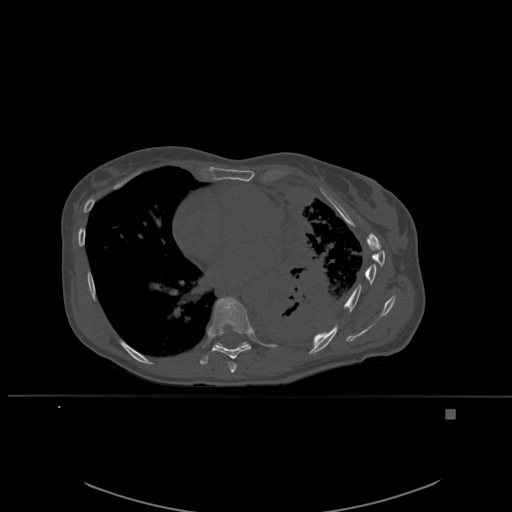
CT including the spine, one axial slice; slice 348 of 537 in the series (ordered by position); bone window (W 1800 / L 400 HU); 512 × 512 image matrix. Patient: female, 45 years. From the clinical record (not read from this slice): primary cancer: lung.
Outlined on this slice (semi-automatically segmented with operator editing):
- T7 vertebra: bounding box <228,361,237,373> (left, top, right, bottom; pixels)
- T8 vertebra: <200,297,251,365>
- T9 vertebra: <214,310,249,347>